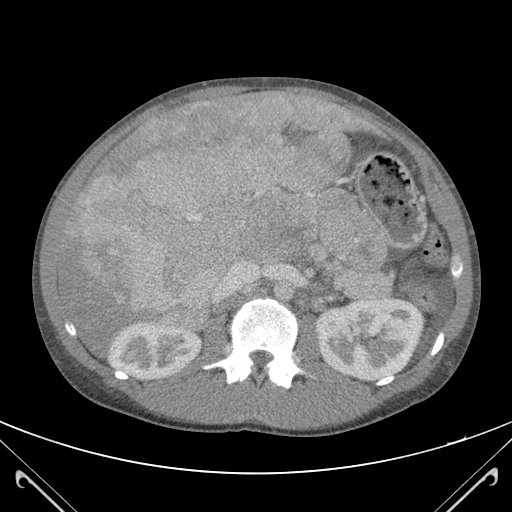
Contrast-enhanced abdominal CT (liver protocol), one axial slice; position 65 of 118 along the scan axis; 120 kVp; soft-tissue window (W 400 / L 40 HU); 512 × 512 image matrix, field of view 380 × 380 mm. From the clinical record (not read from this slice): diagnosis: hepatocellular carcinoma (patient treated with transarterial chemoembolisation; whether this scan precedes or follows treatment is not stated here); TNM stage (as recorded): Stage-IIIB; Child-Pugh class: A; tumour nodularity: uninodular.
Outlined on this slice (semi-automatically segmented with operator editing):
- abdominal aorta: bounding box [x1, y1, x2, y2] px = [274, 279, 294, 302]
- liver parenchyma outside the tumour (the mass and vessels are separate outlines, so this box may not span the whole liver): [57, 92, 360, 354]
- mass: [62, 93, 358, 331]
- liver vessels: [212, 106, 349, 302]